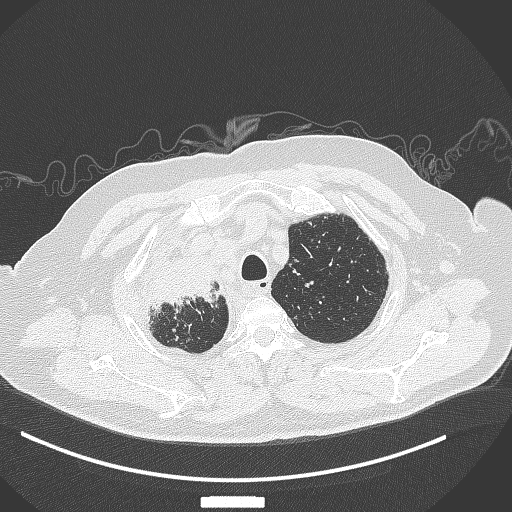
Chest CT, one axial slice; 120 kVp; lung window (W 1500 / L -600 HU); 1 mm slice thickness; 512 × 512 image matrix. Male patient, age 69 years. From the clinical record (not read from this slice): clinical TNM (as recorded): T4 N3 M1.
Structures marked on this image (rectangle marked by the reading radiologist):
- lung tumour (recorded histology: adenocarcinoma): bounding box [x1, y1, x2, y2] px = [147, 257, 219, 314]